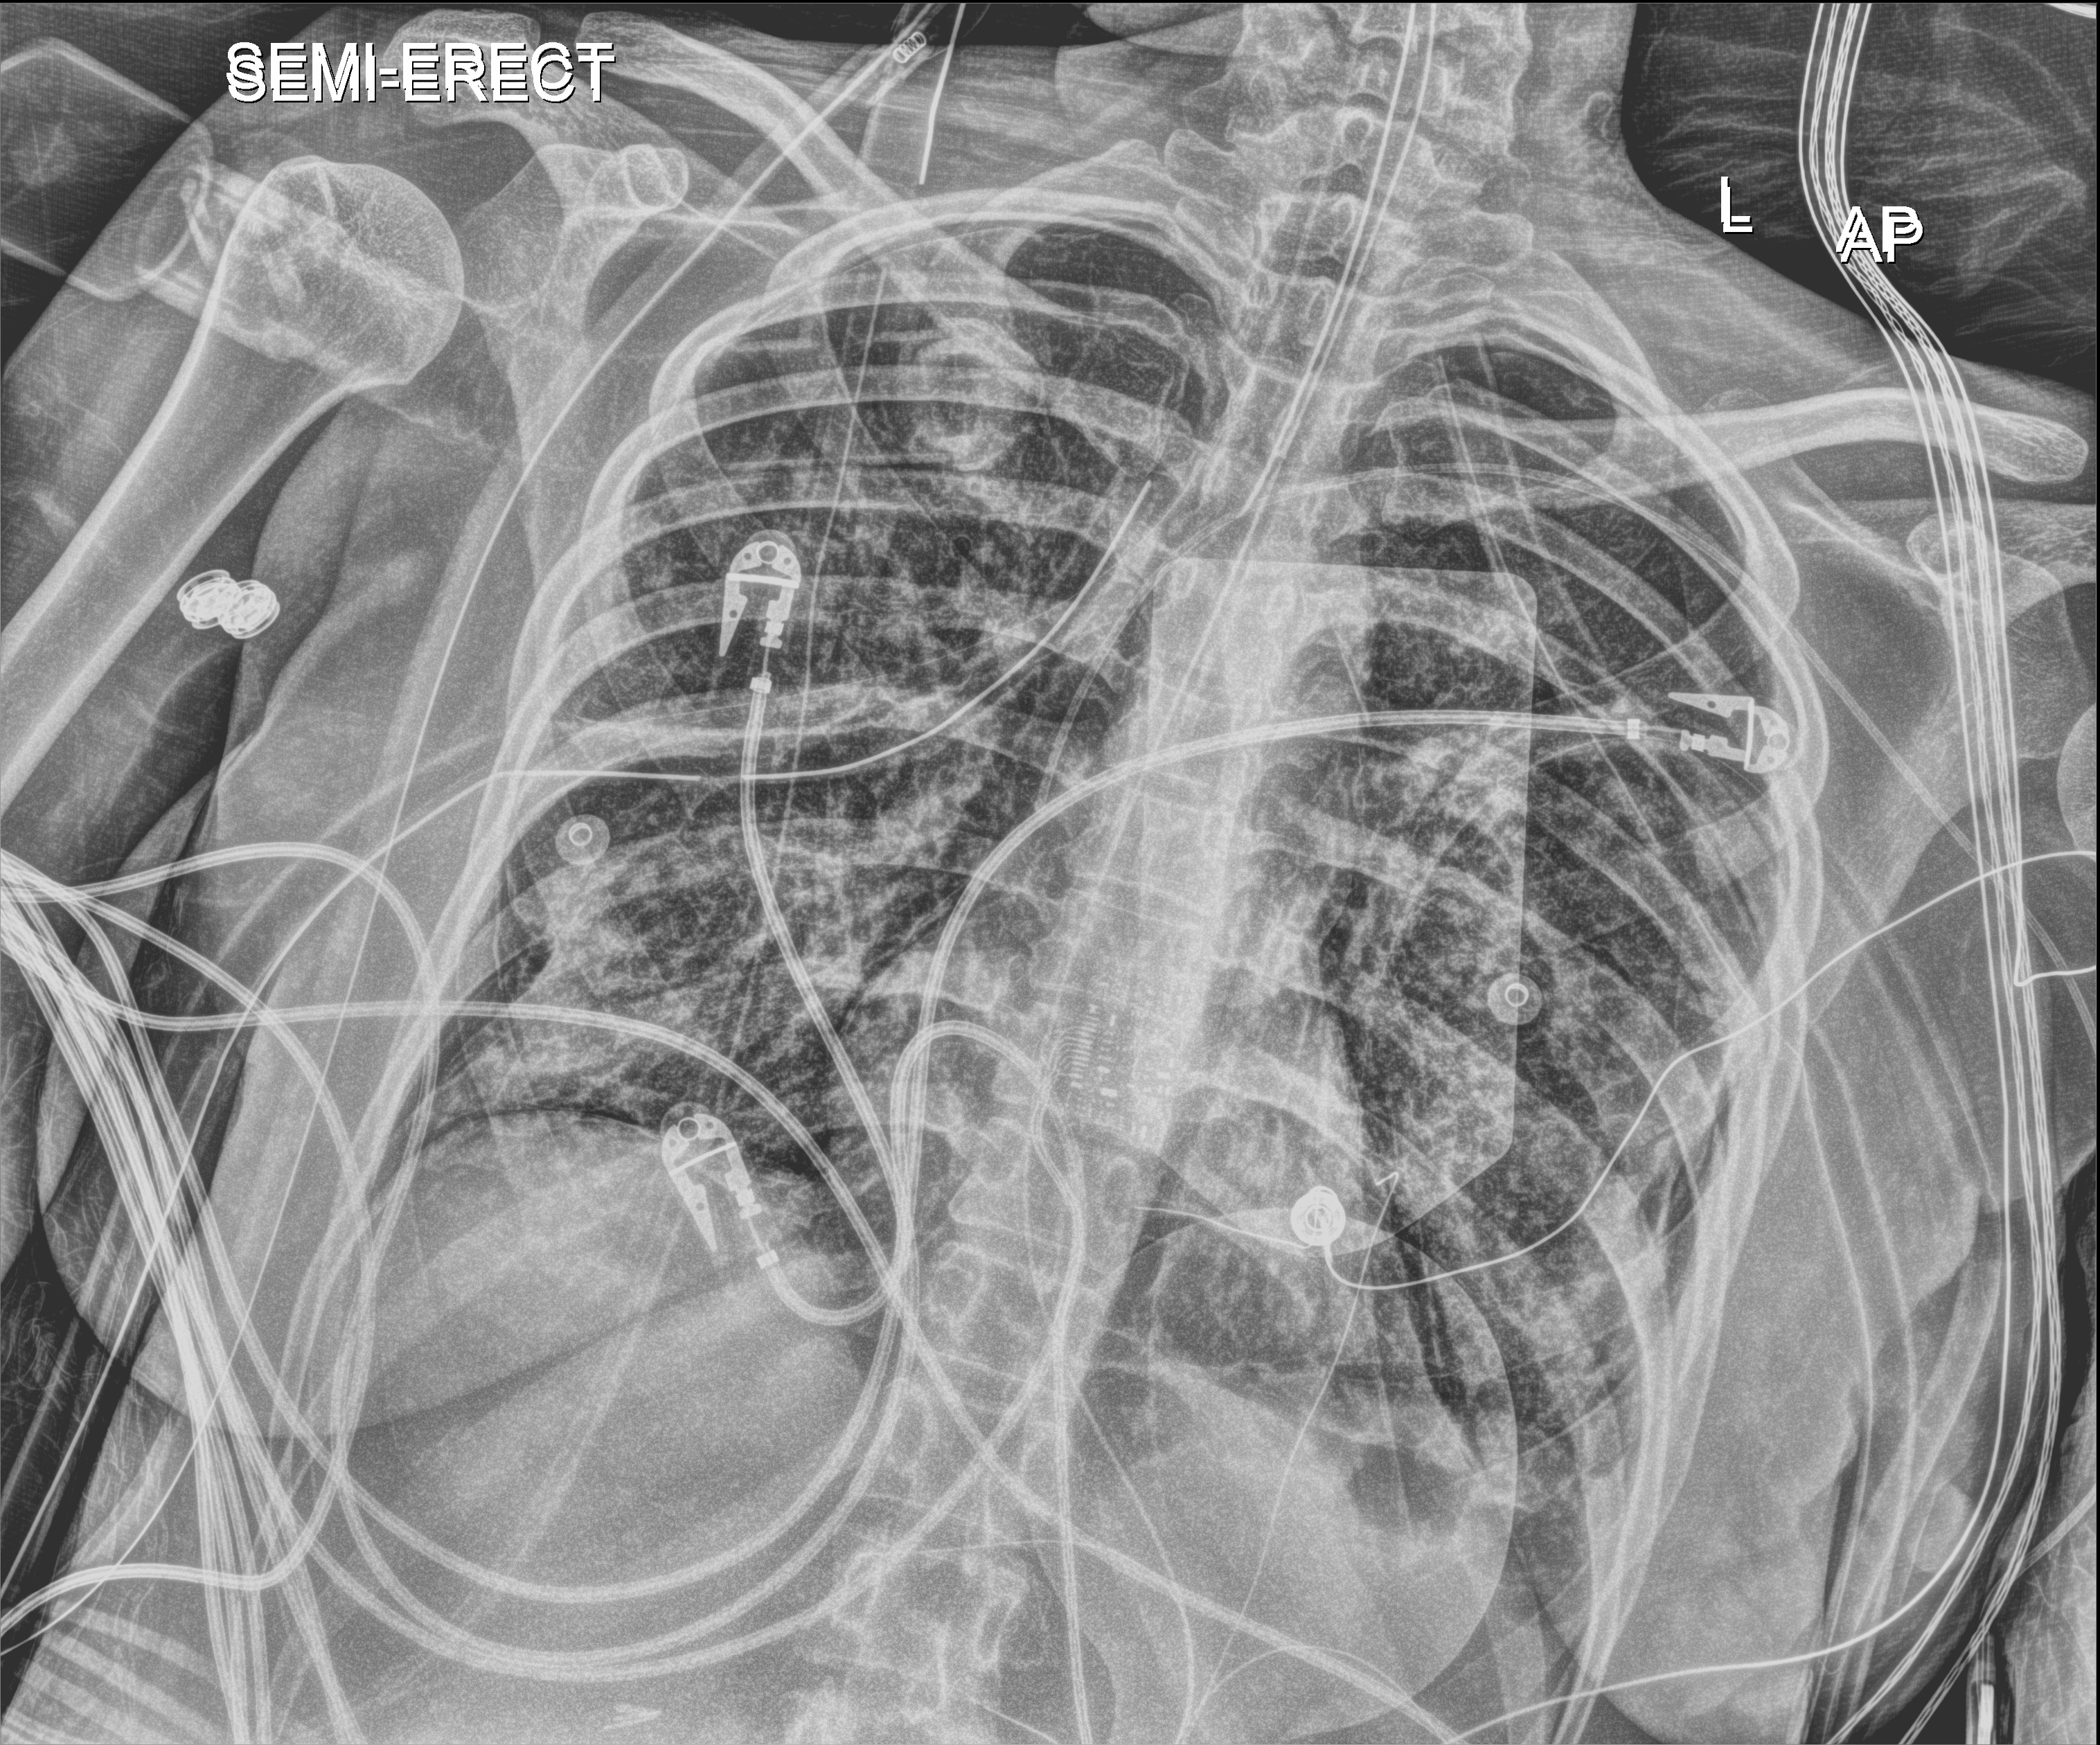
Bedside chest radiograph (digital radiography); anteroposterior (AP) projection. Adult patient hospitalised with COVID-19, age 18–59 years.
Hospital-stay facts (about this admission, not read from this image; timing relative to this image not recorded): chronic kidney disease (admission record): no; mechanically ventilated during this hospital stay: yes; admitted to intensive care during this hospital stay: yes.